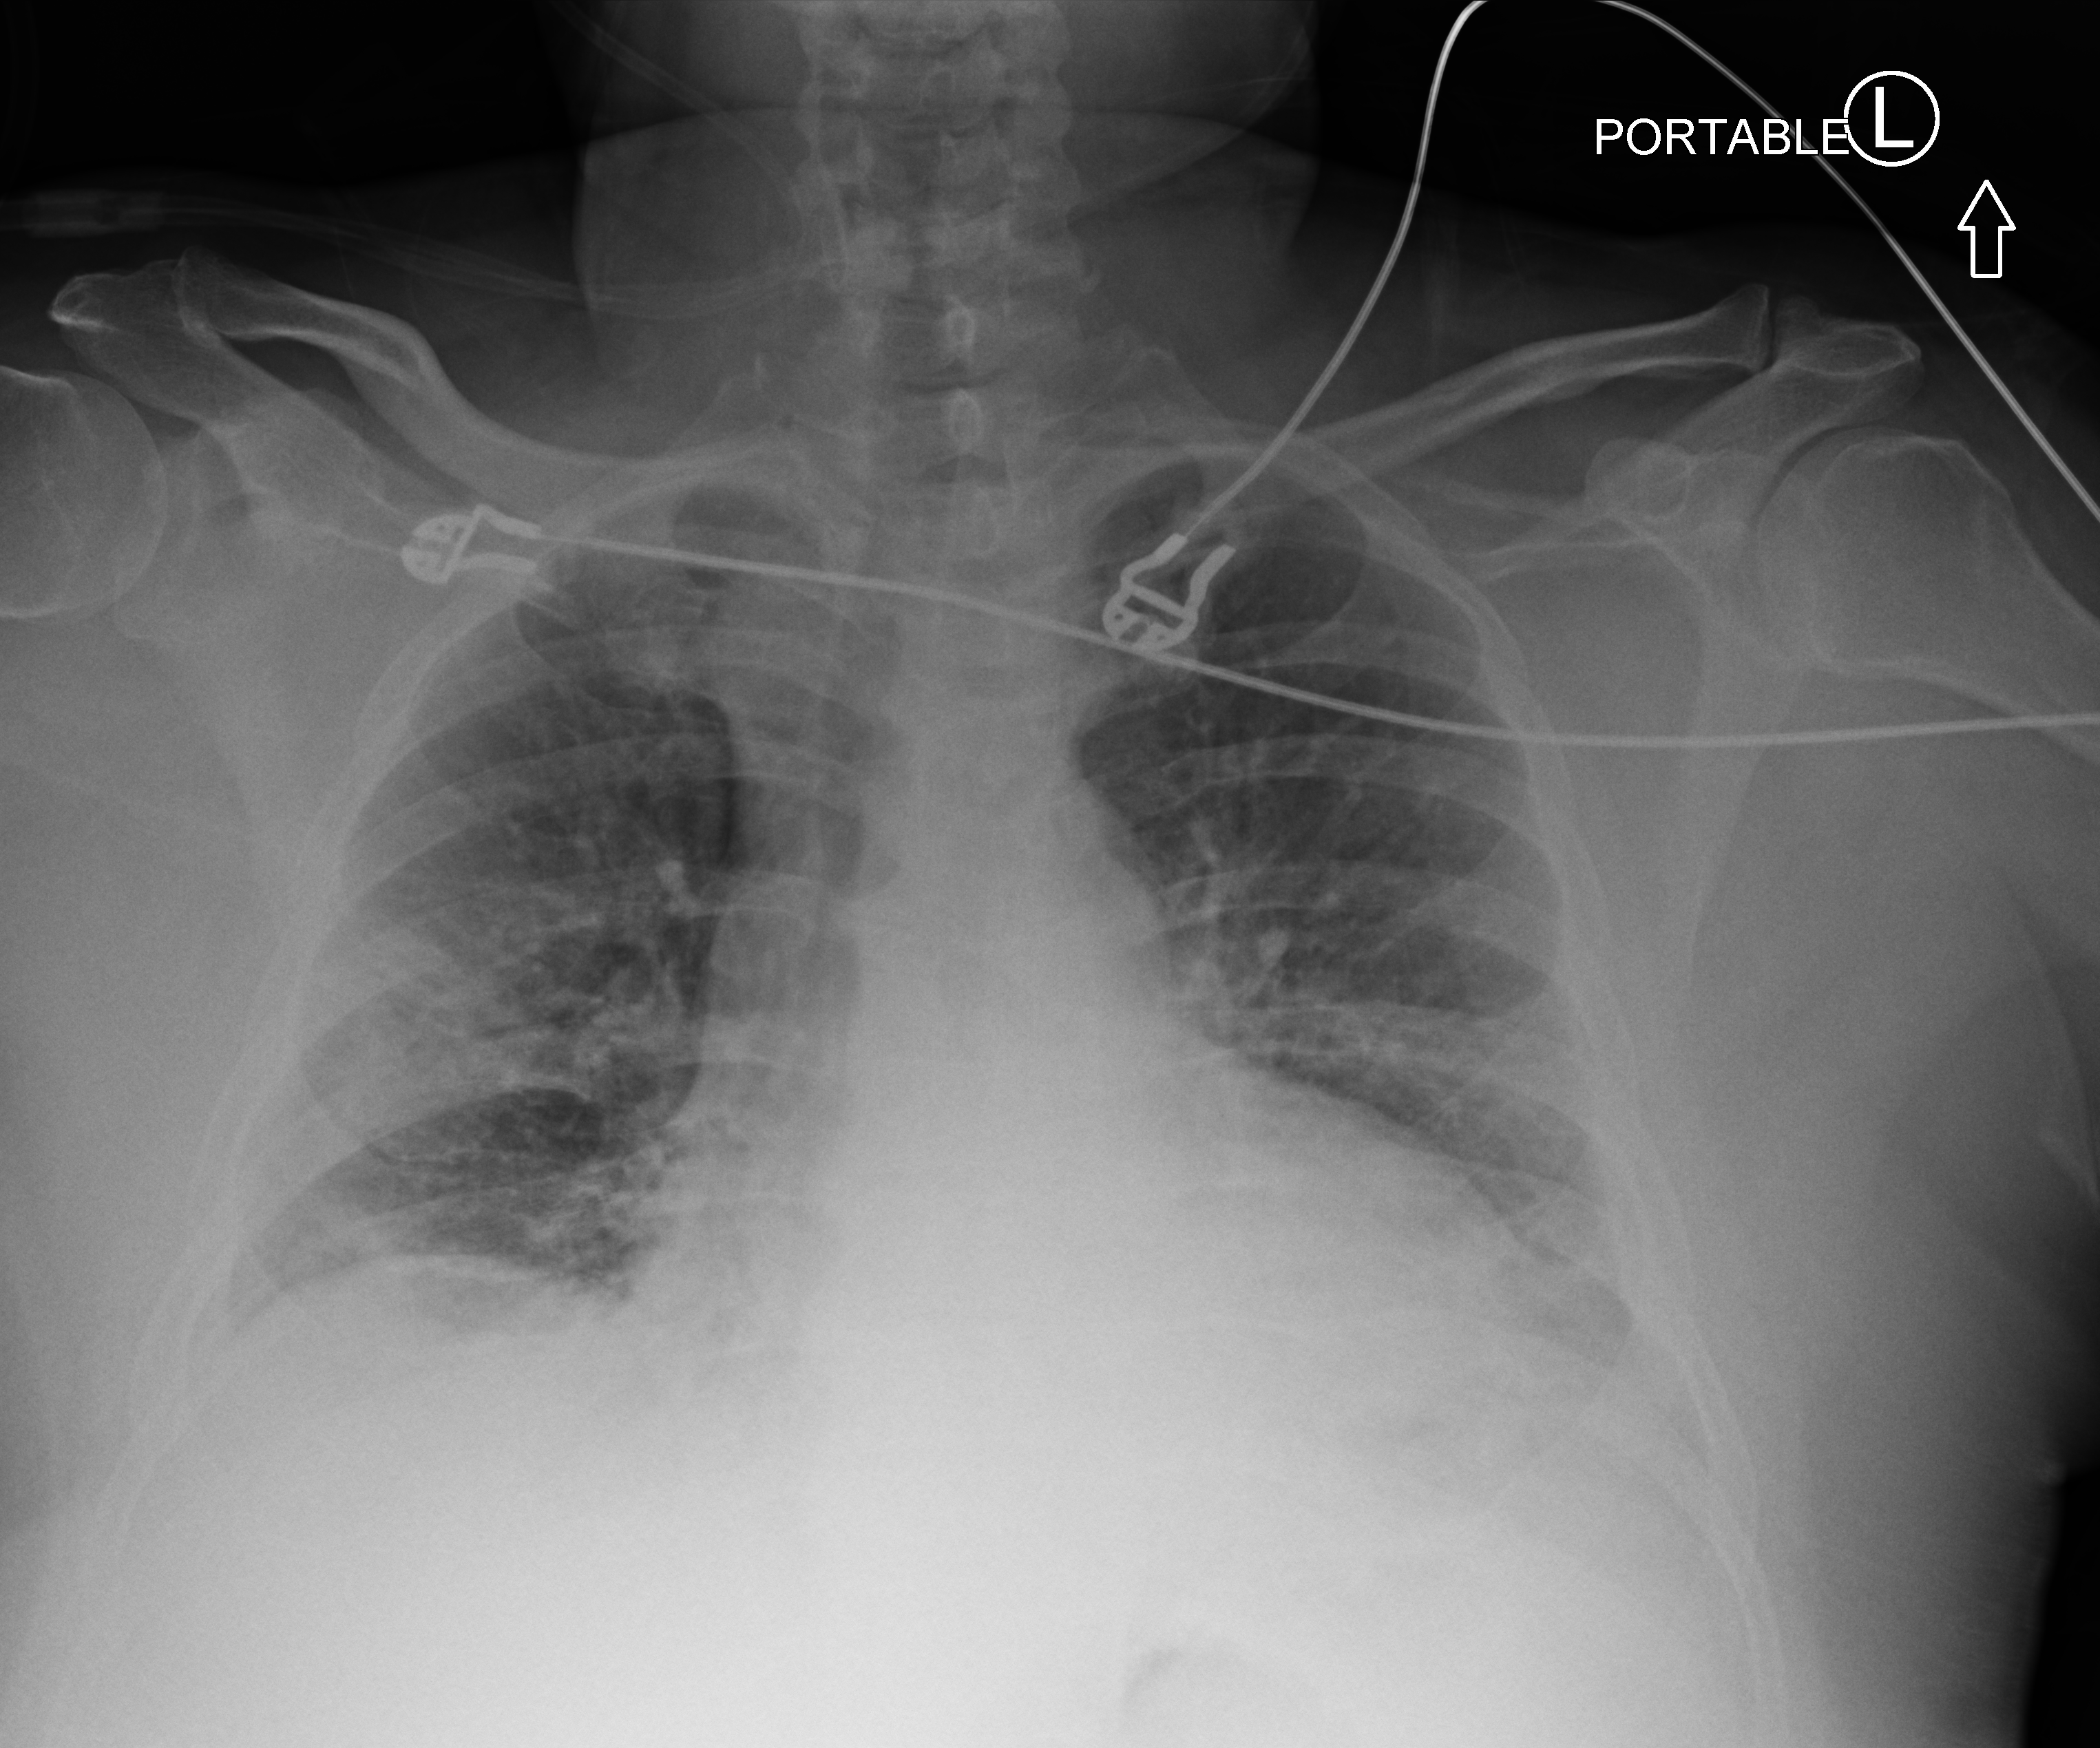
Portable chest radiograph; anteroposterior (AP) projection. Male patient hospitalised with COVID-19, age 18–59 years.
Admission-level facts for this patient (not findings on this image; timing relative to this image not recorded): admitted to intensive care during this hospital stay: yes; mechanically ventilated during this hospital stay: yes; other chronic lung disease (admission record): no.